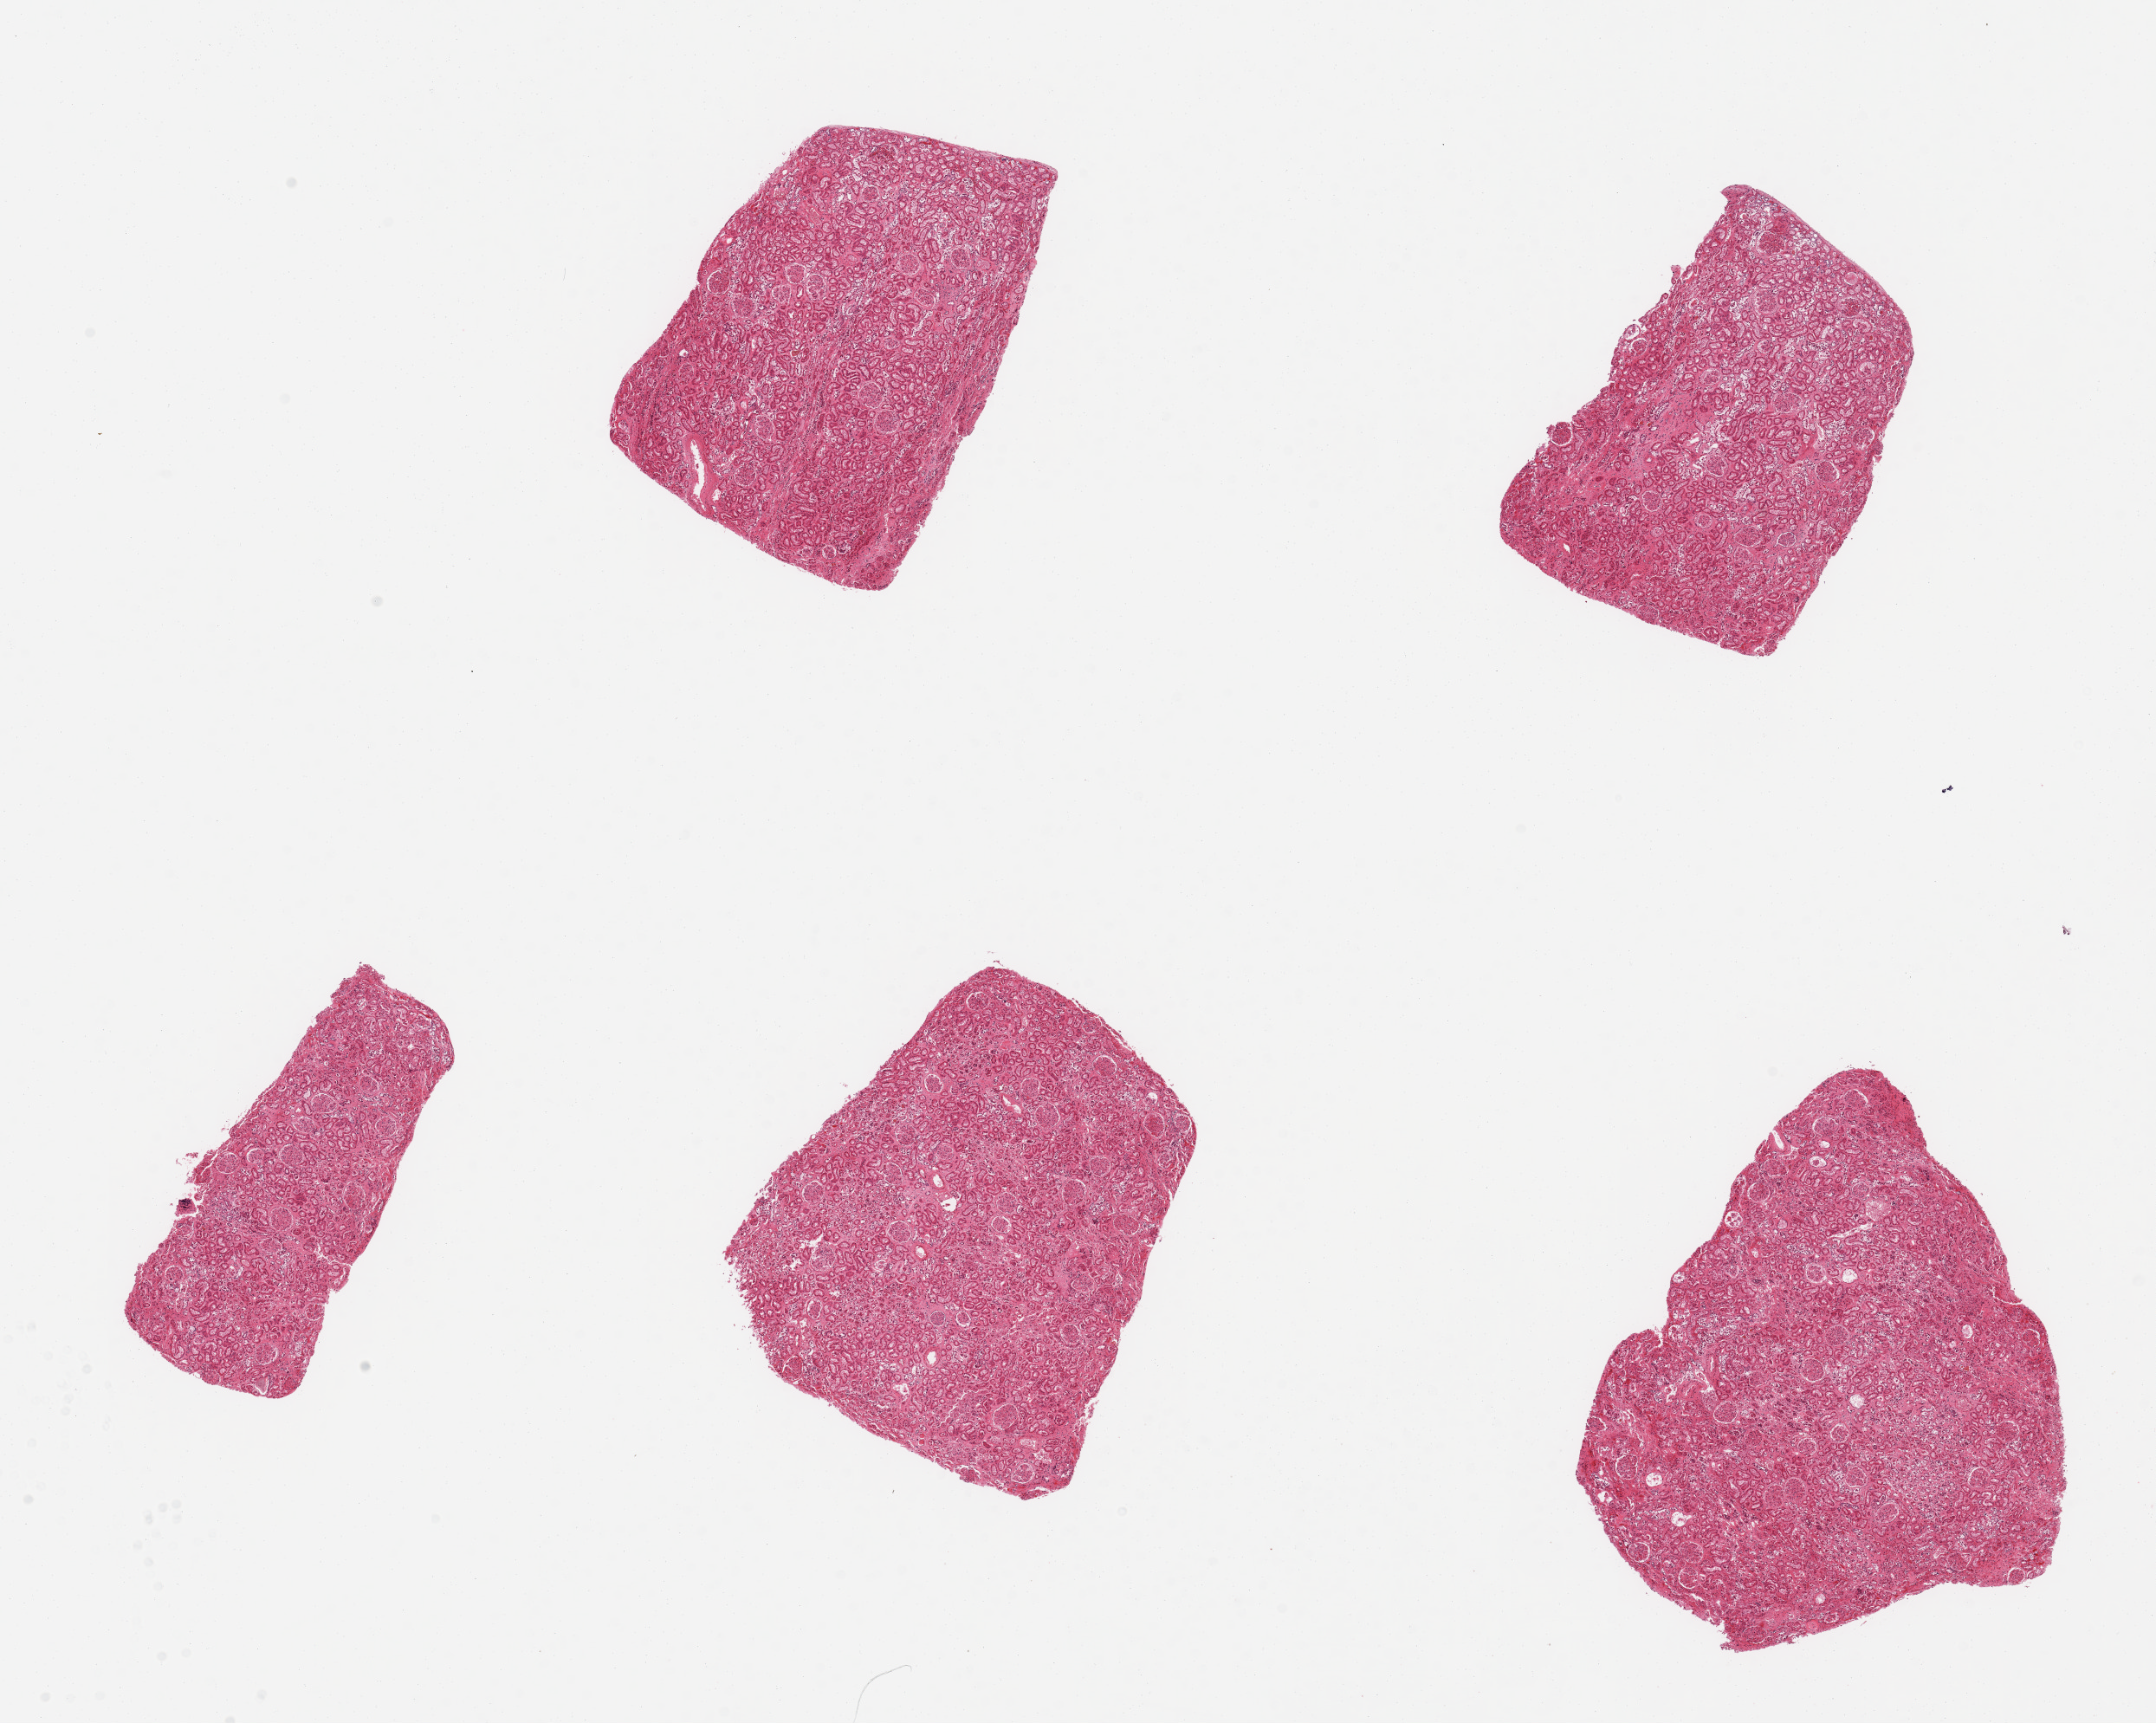
Whole-slide image, haematoxylin and eosin stain — low-resolution overview of the scanned area, about 19.7 x 15.7 mm; PAXgene-fixed paraffin-embedded (PFPE) section; target tissue: renal cortex; tissue donor sample. Donor sex: male.
Review note (as recorded): 5 pieces, glomeruli present.